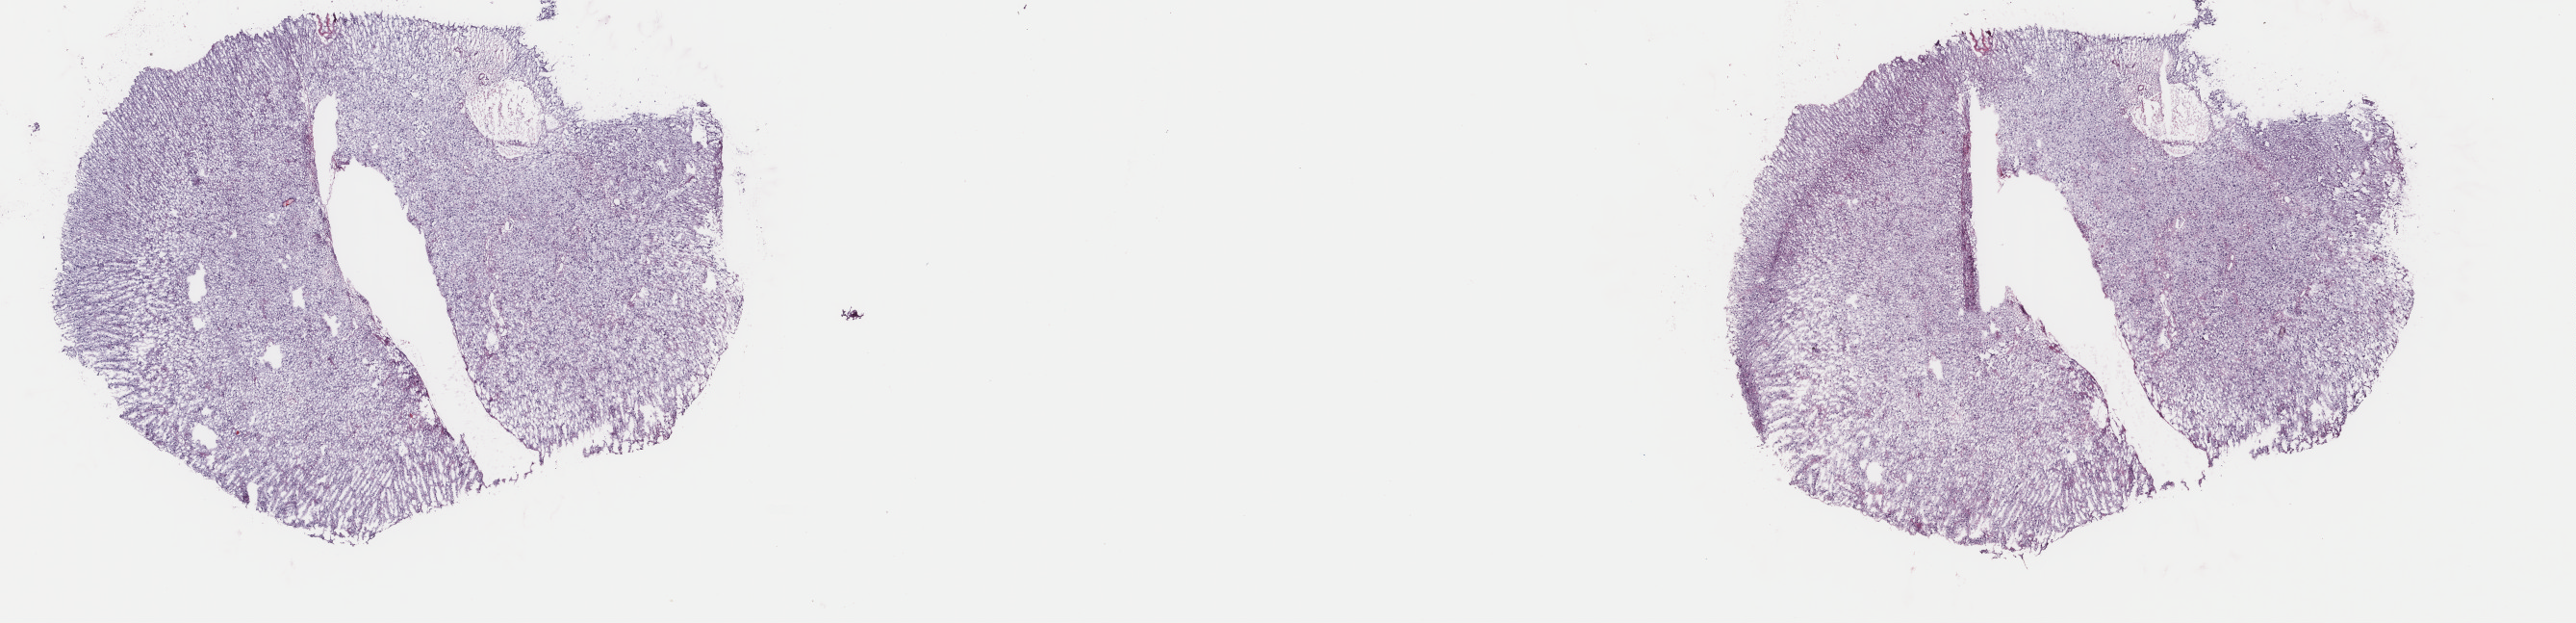
Digitized Hematoxylin and eosin (H&E) stained tissue section (whole slide) — a low-resolution overview of the entire scanned area, about 21.2 x 5.1 mm; frozen section; sample: primary tumour, brain. Female patient; age at initial diagnosis 44 years. Histologic grade: G2 (moderately differentiated). Pathologist review of this section (percent, as recorded): tumour cells 50%, tumour nuclei 80%, normal cells 10%, stromal cells 40%, necrosis 0%. Infiltration values recorded for this section: lymphocyte infiltration 0%, monocyte infiltration 0%, neutrophil infiltration 0%.
* diagnosis: Oligodendroglioma, NOS (cerebrum)